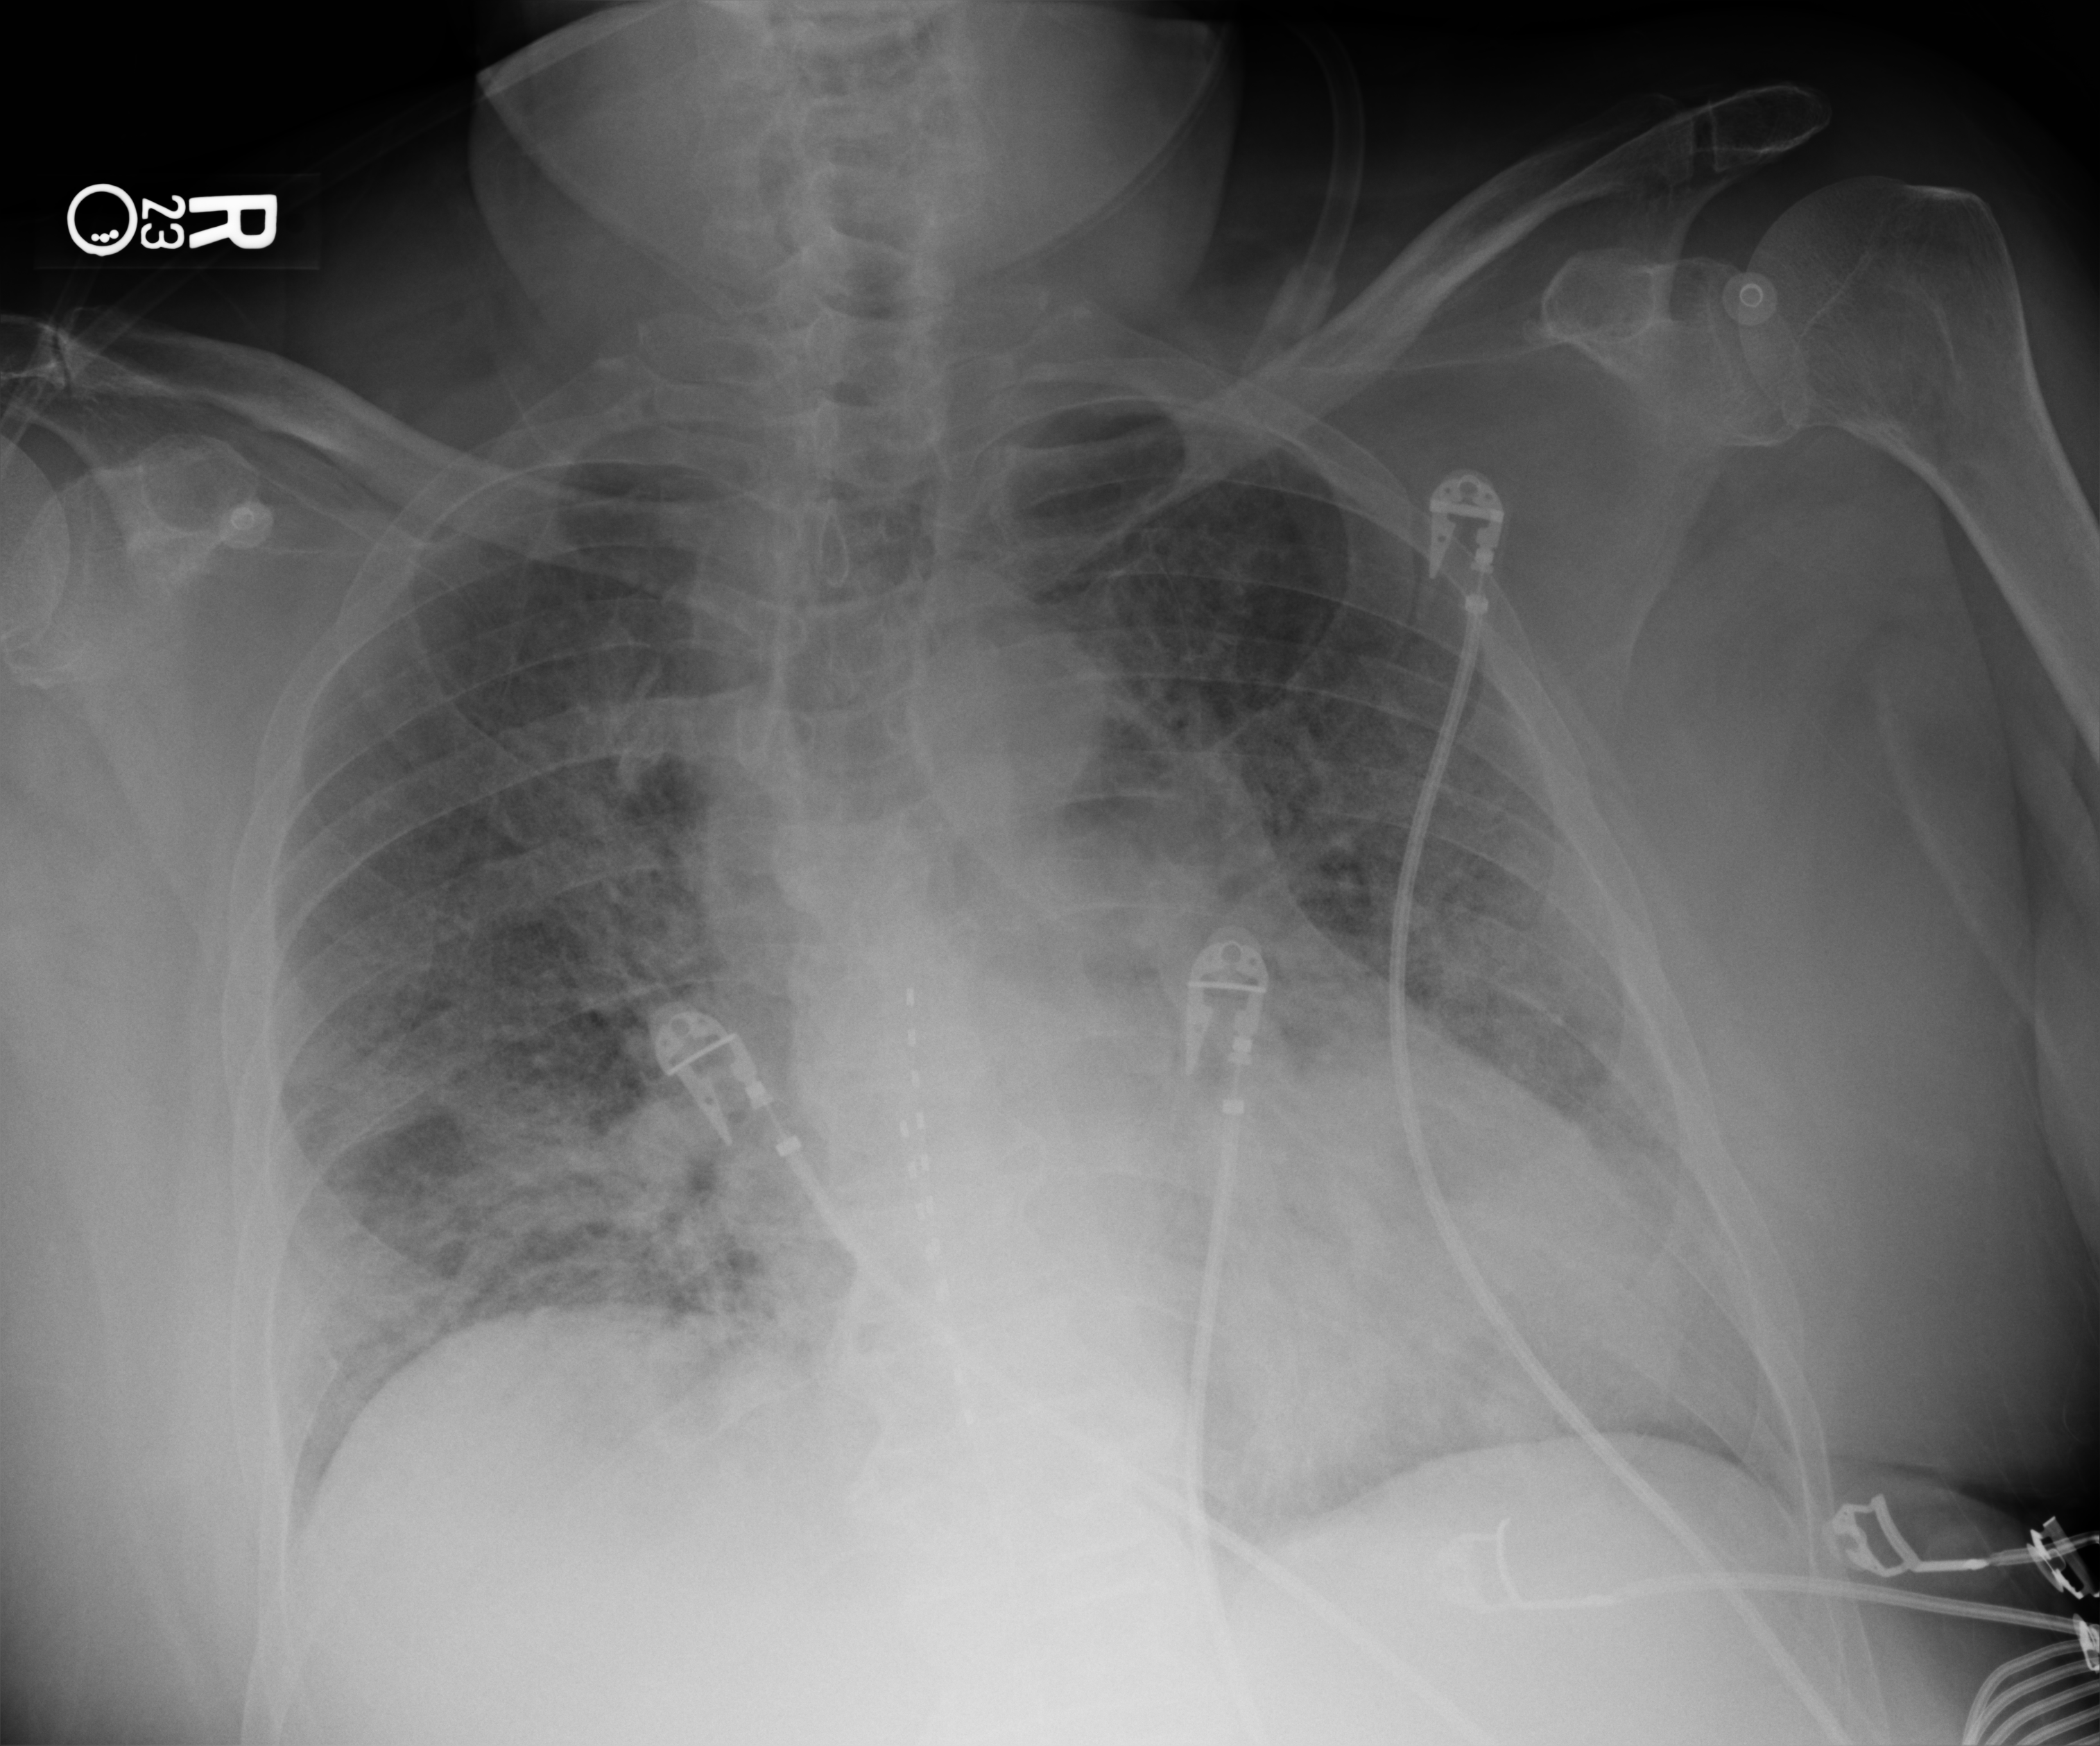
Portable chest radiograph; anteroposterior (AP) projection. Patient hospitalised with COVID-19; male, aged 60–74 years.
Admission-level facts for this patient (not findings on this image; timing relative to this image not recorded): smoking status (admission record): never; diabetes (admission record): no; mechanically ventilated during this hospital stay: no.